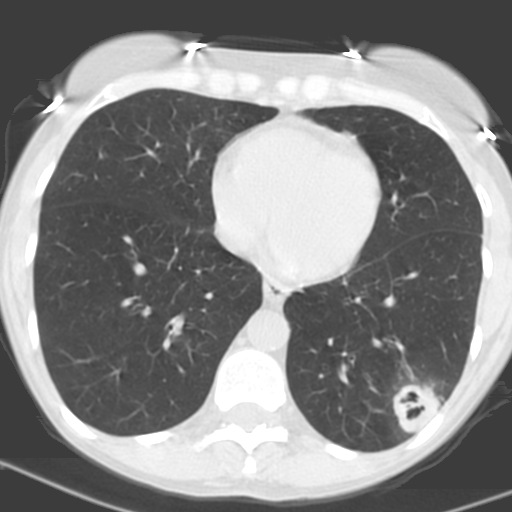
Low-dose screening chest CT, one axial slice; slice 58 of 156 in the series (ordered by position); lung window (W 1500 / L -600 HU); 512 × 512 image matrix.
Outlined on this slice (outlined manually by an expert reader):
- lesion 1 (tumor, lower lobe of left lung): bounding box [x1, y1, x2, y2] px = [393, 383, 440, 435]